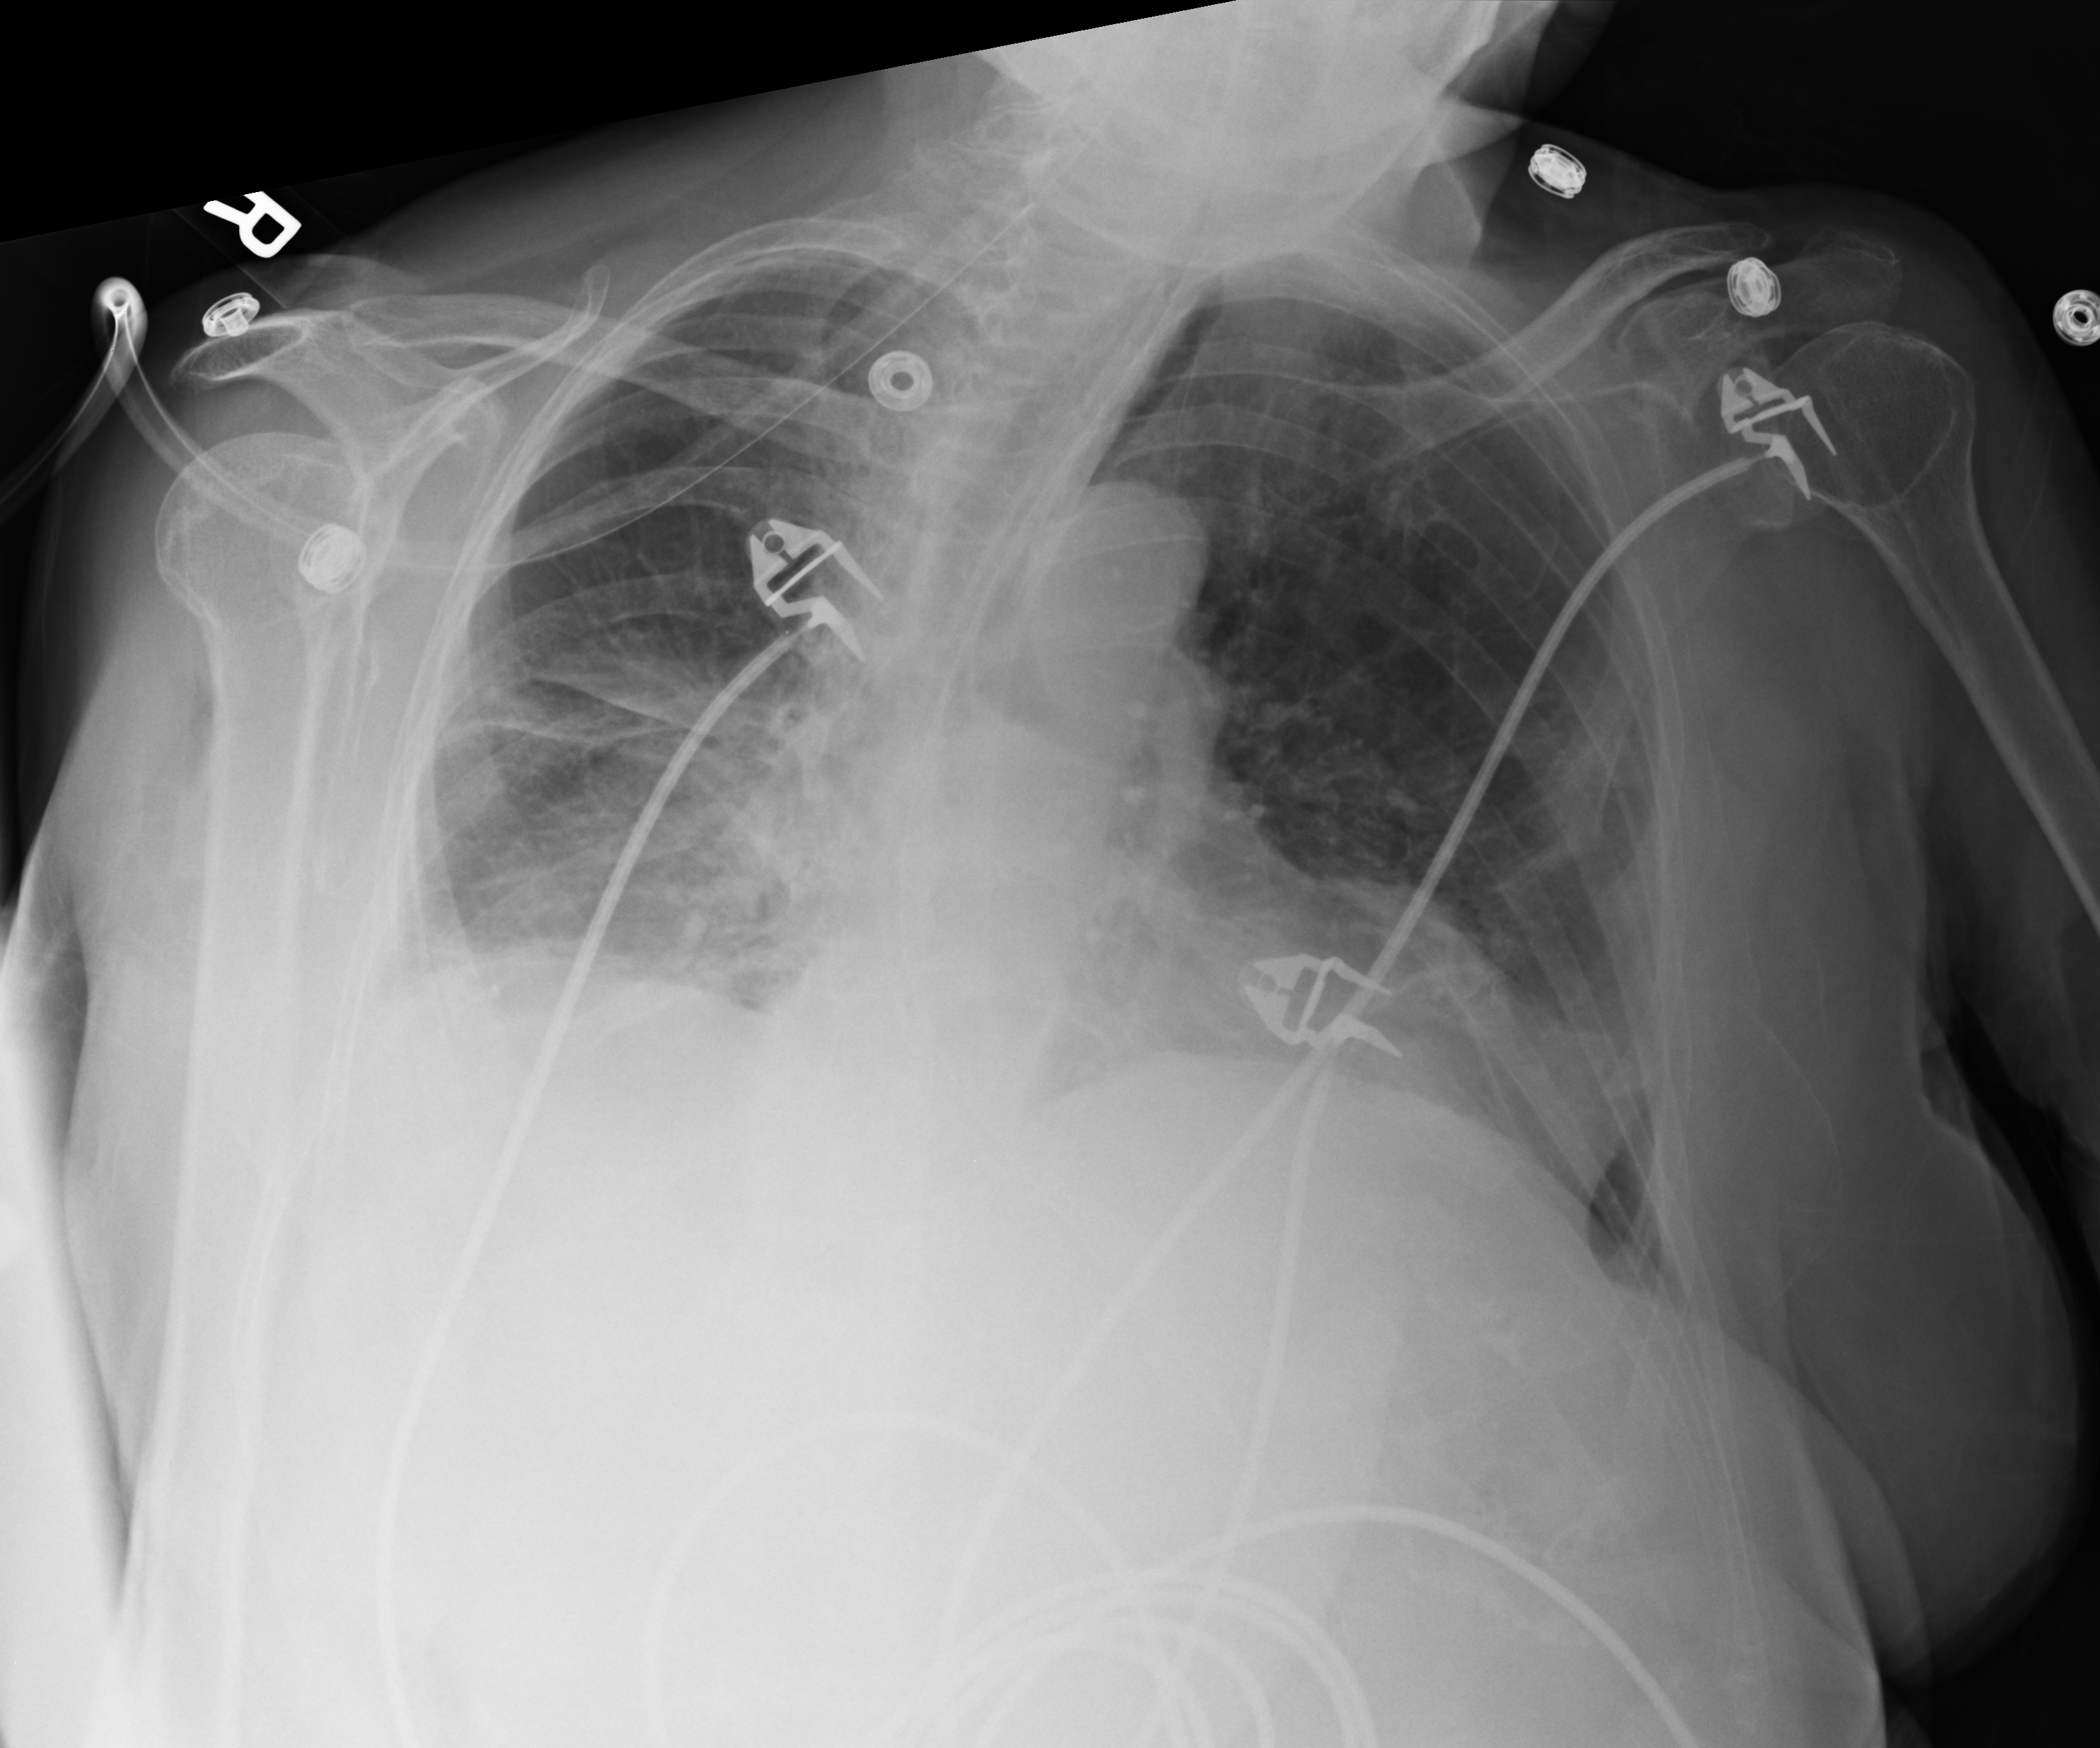
Bedside chest radiograph (computed radiography), anteroposterior (AP) projection. Female patient hospitalised with COVID-19, age 75–90 years.
Hospital-stay facts (about this admission, not read from this image; timing relative to this image not recorded): mechanically ventilated during this hospital stay: yes.